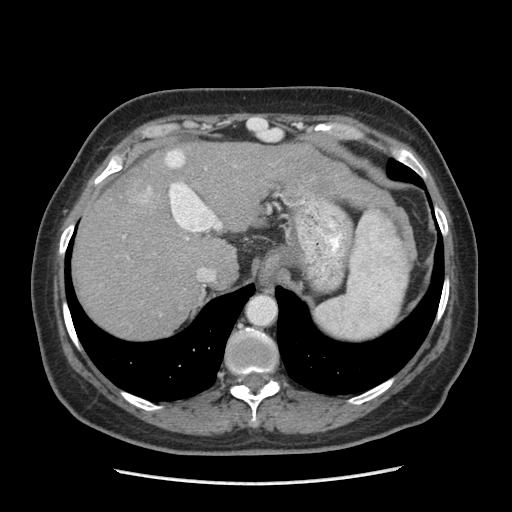
Contrast-enhanced abdominal CT (liver protocol), one axial slice. Slice 163 of 185 in the series (ordered by position). Reconstruction kernel STANDARD. 140 kVp. Soft-tissue window (W 400 / L 40 HU). 2.5 mm slice thickness. 512 × 512 image matrix. From the clinical record (not read from this slice): diagnosis: hepatocellular carcinoma (patient treated with transarterial chemoembolisation; whether this scan precedes or follows treatment is not stated here); TNM stage (as recorded): Stage-I; Child-Pugh class: A; tumour differentiation: poorly differentiated.
Annotated regions visible in this slice (semi-automatic segmentation, software-assisted and operator-edited):
- abdominal aorta: bounding box <247,296,275,324> (left, top, right, bottom; pixels)
- liver parenchyma outside the tumour (the mass and vessels are separate outlines, so this box may not span the whole liver): <72,142,335,338>
- mass: <127,174,164,212>